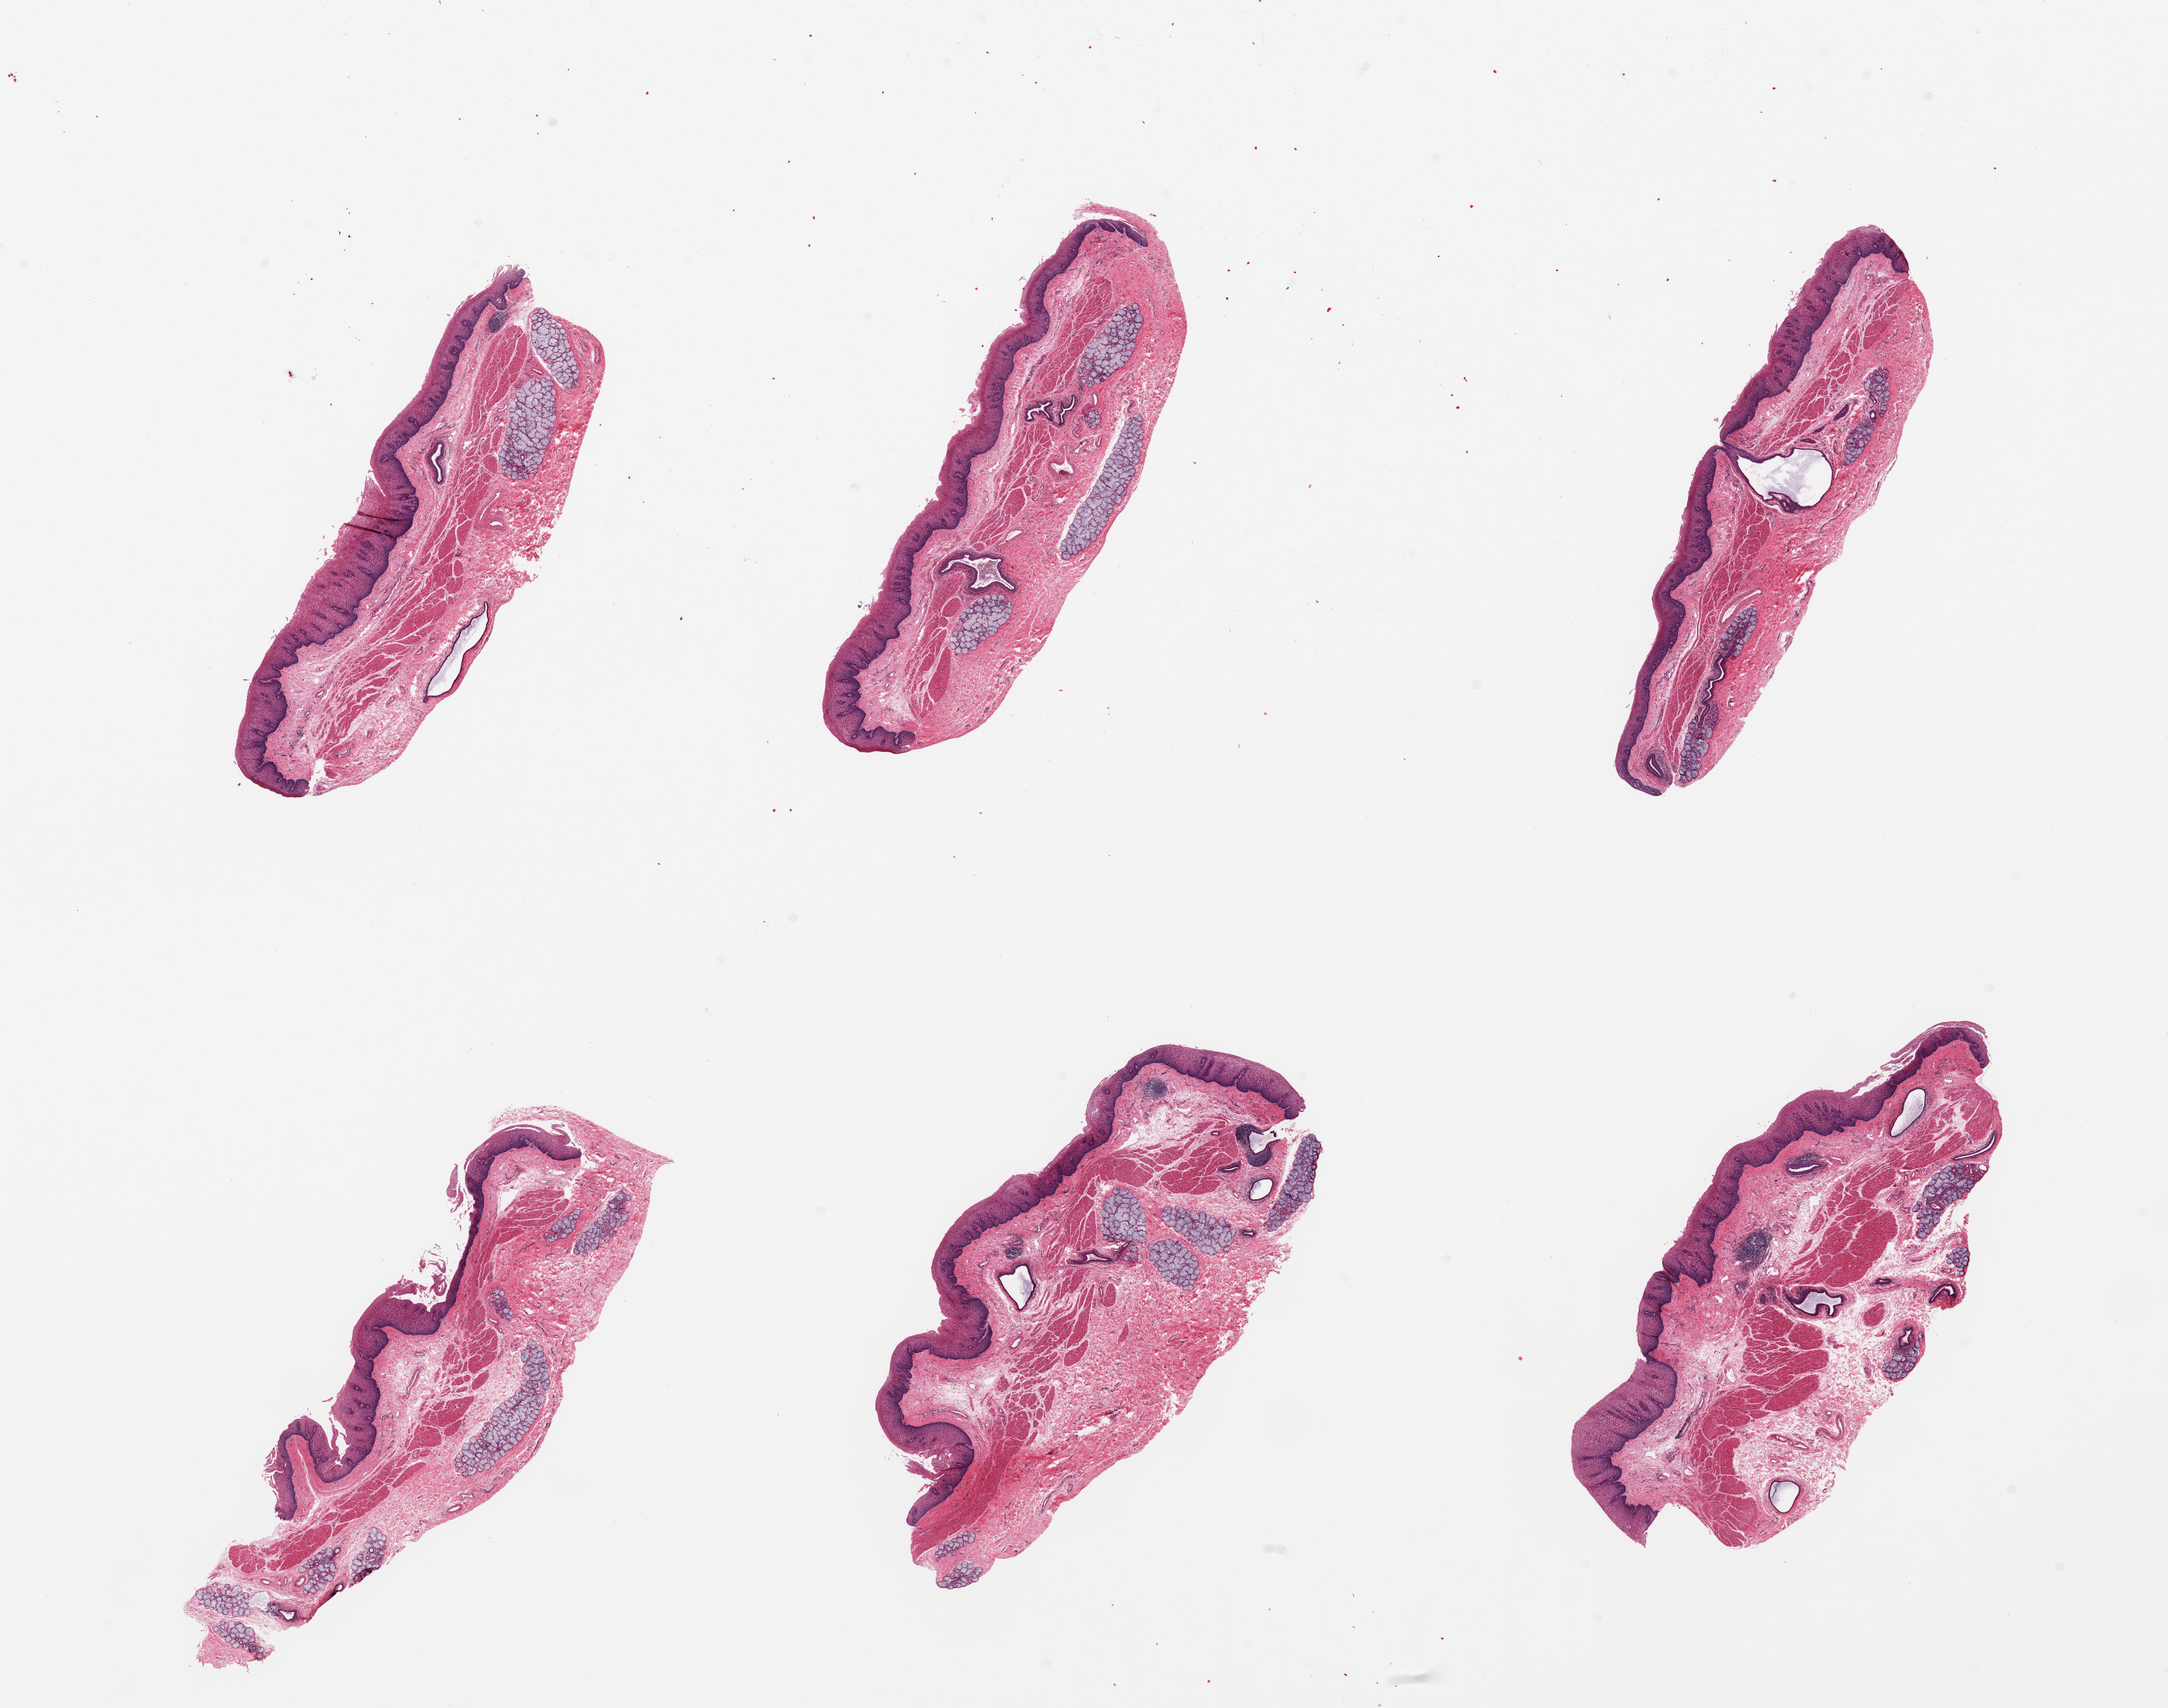
Digitized H&E-stained section — whole scanned area (about 22.6 x 17.8 mm) shown as a low-resolution overview, PAXgene-fixed, paraffin-embedded tissue, sampled site (target tissue): esophageal mucous membrane, tissue donor sample. Donor: male.
Reviewer comment on this tissue sample: 6 pieces; submucosal glands and ducts are prominent making up 10%.